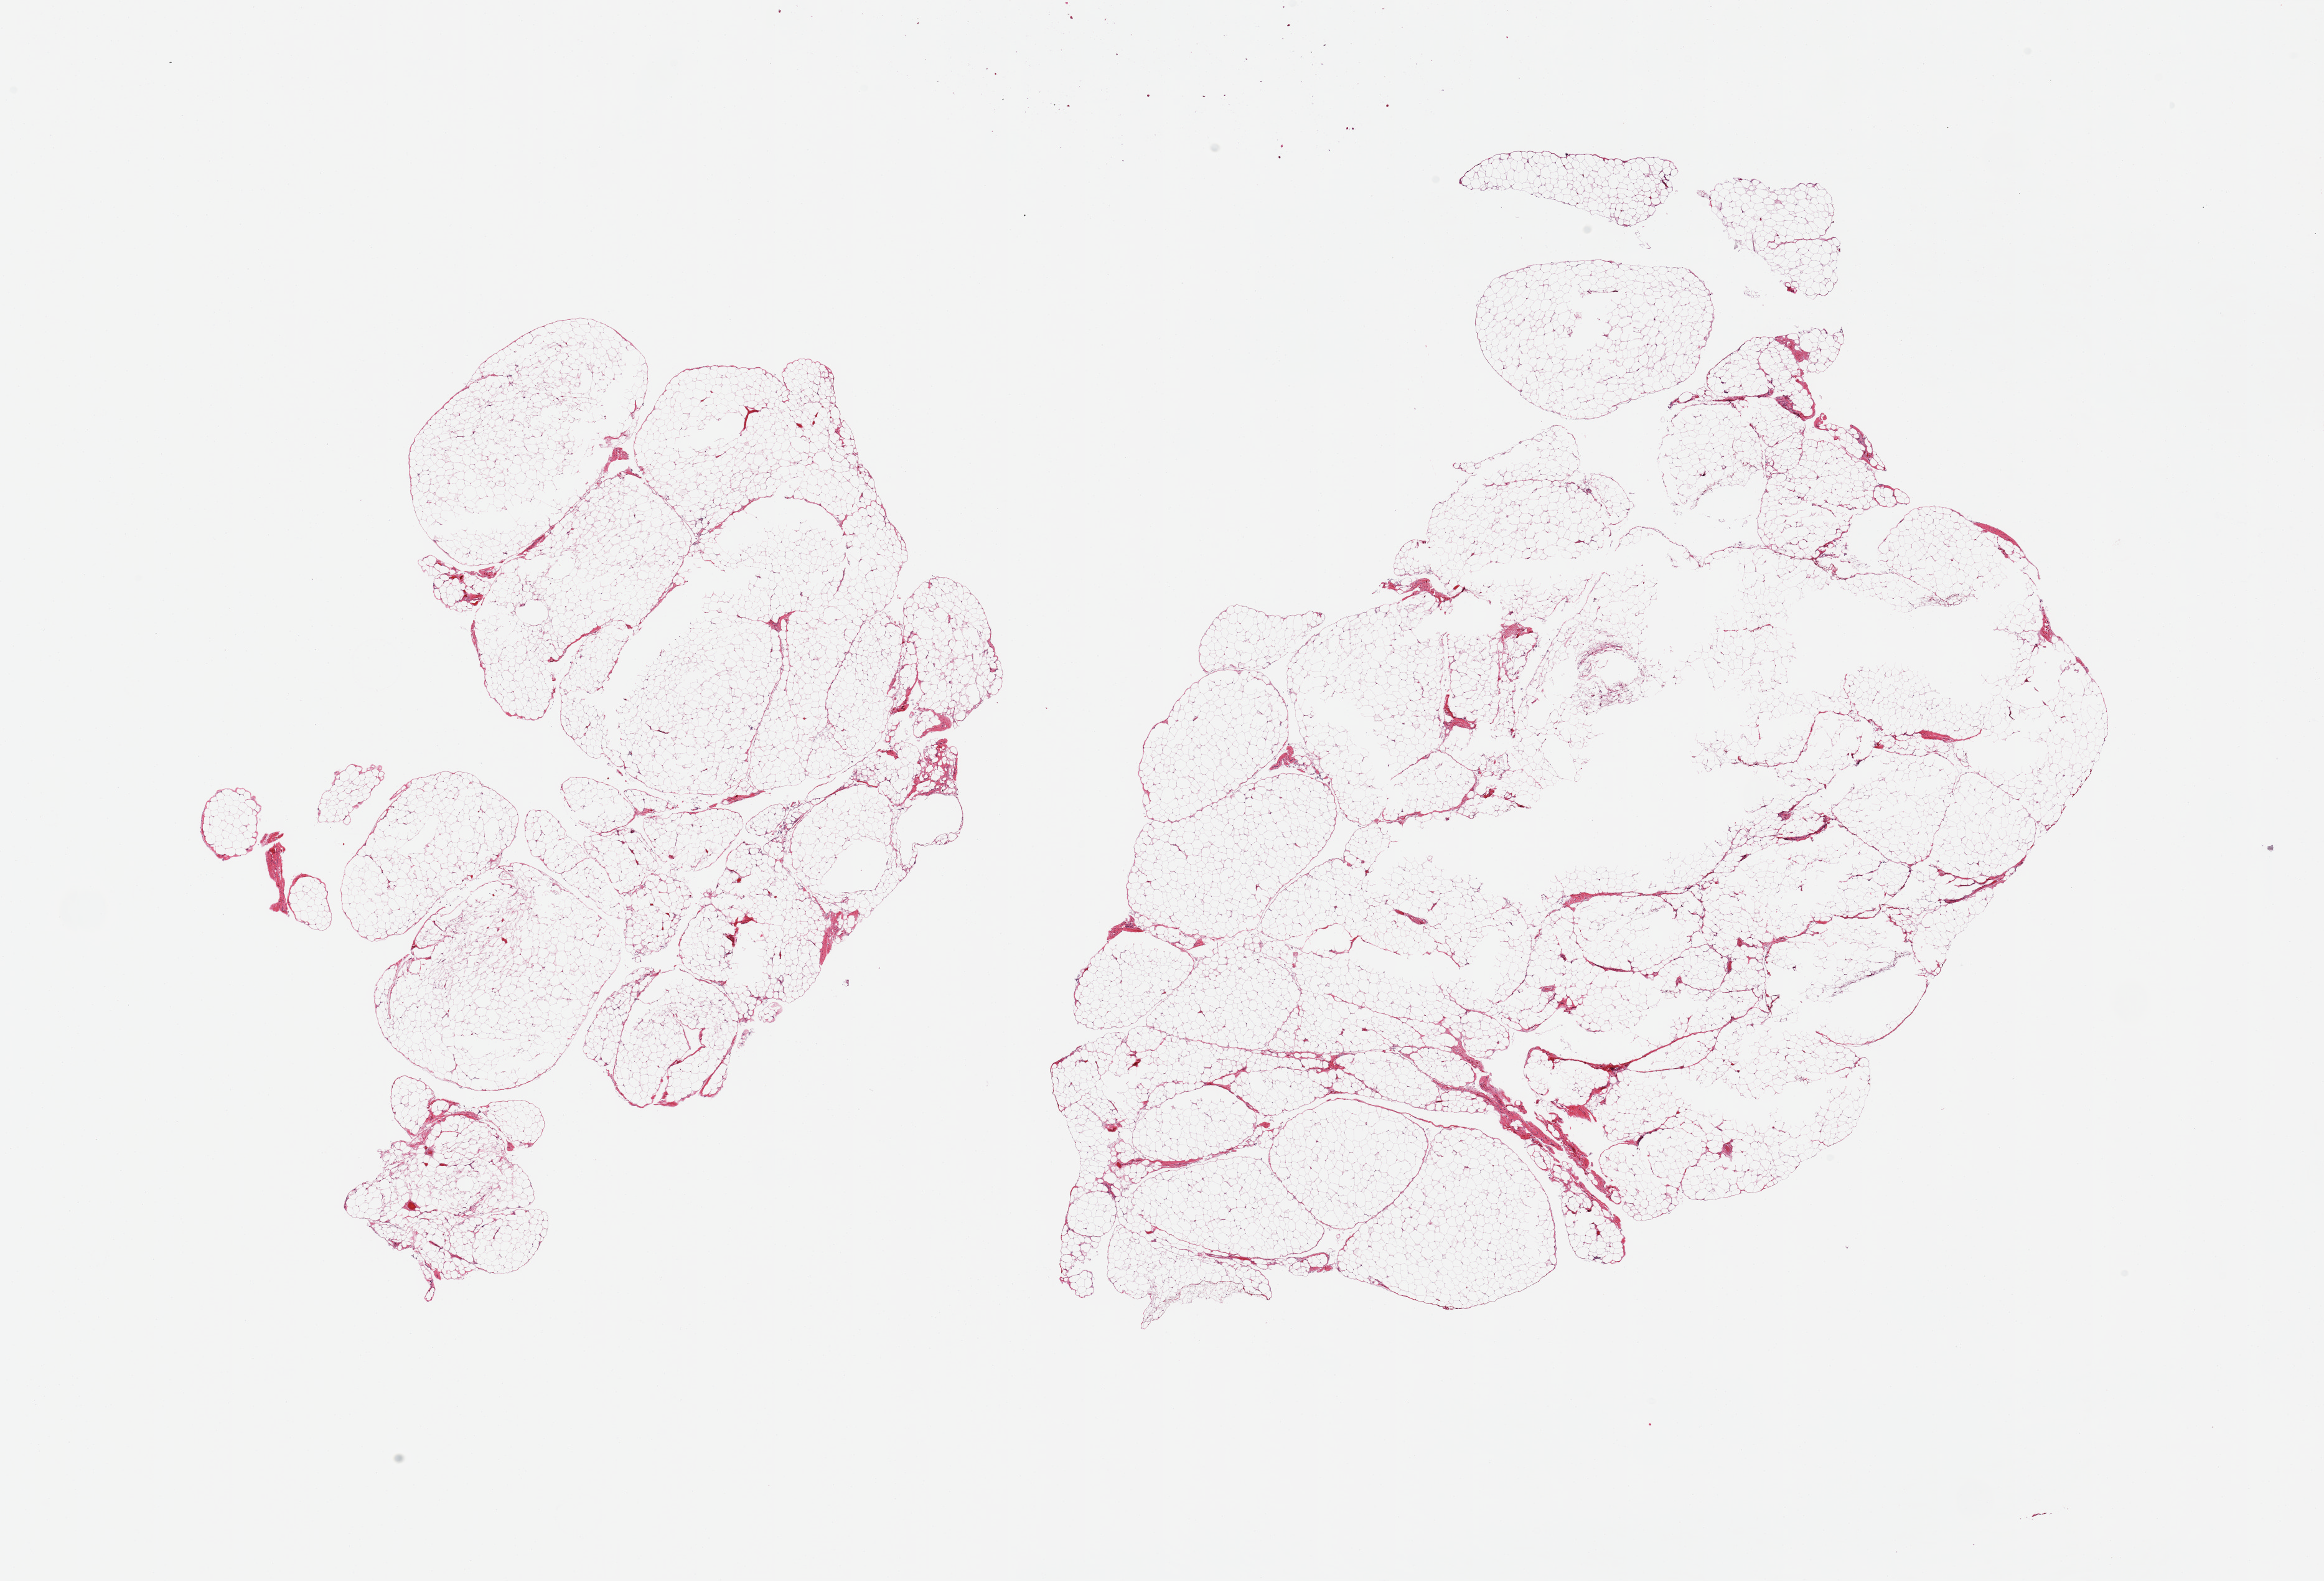
Whole-slide image, H&E stain, low-resolution overview of the scanned area, about 29.5 x 20.1 mm (slide scanned at 20x); PAXgene-fixed, paraffin-embedded tissue; sampled site (target tissue): omentum; tissue donor sample. Donor sex: male.
* review note (as recorded): 2 pieces; lobulated adipose tissue, small central defects